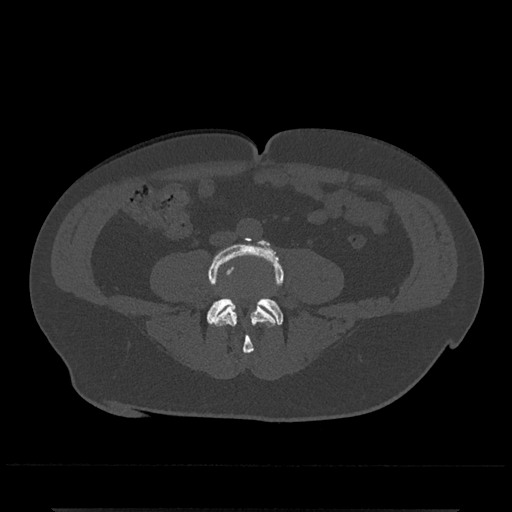
CT including the spine, one axial slice; position 125 of 797 along the scan axis; reconstruction kernel Br40s/3; bone window (W 1800 / L 400 HU); 0.5 mm slice thickness; 512 × 512 image matrix, field of view 393 × 393 mm. Male patient, age 67 years. From the clinical record (not read from this slice): primary cancer: prostate.
Annotated regions visible in this slice (semi-automatically segmented with operator editing):
- L4 vertebra: box from (x=208, y=240) to (x=283, y=354) px
- L5 vertebra: (x=207, y=297)–(x=283, y=324)